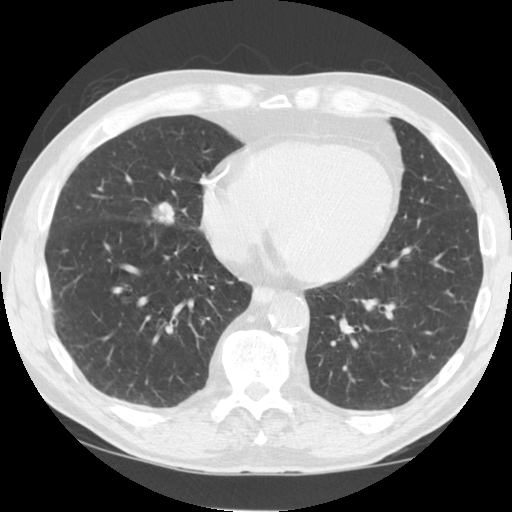
Low-dose screening chest CT, one axial slice. Slice 39 of 125 in the series (ordered by position). 120 kVp. Lung window (W 1500 / L -600 HU). 512 × 512 image matrix.
Annotated regions visible in this slice (expert manual segmentation):
- lesion 1 (tumor, middle lobe of right lung): bounding box (x1, y1, x2, y2) in pixels: (152, 202, 174, 223)